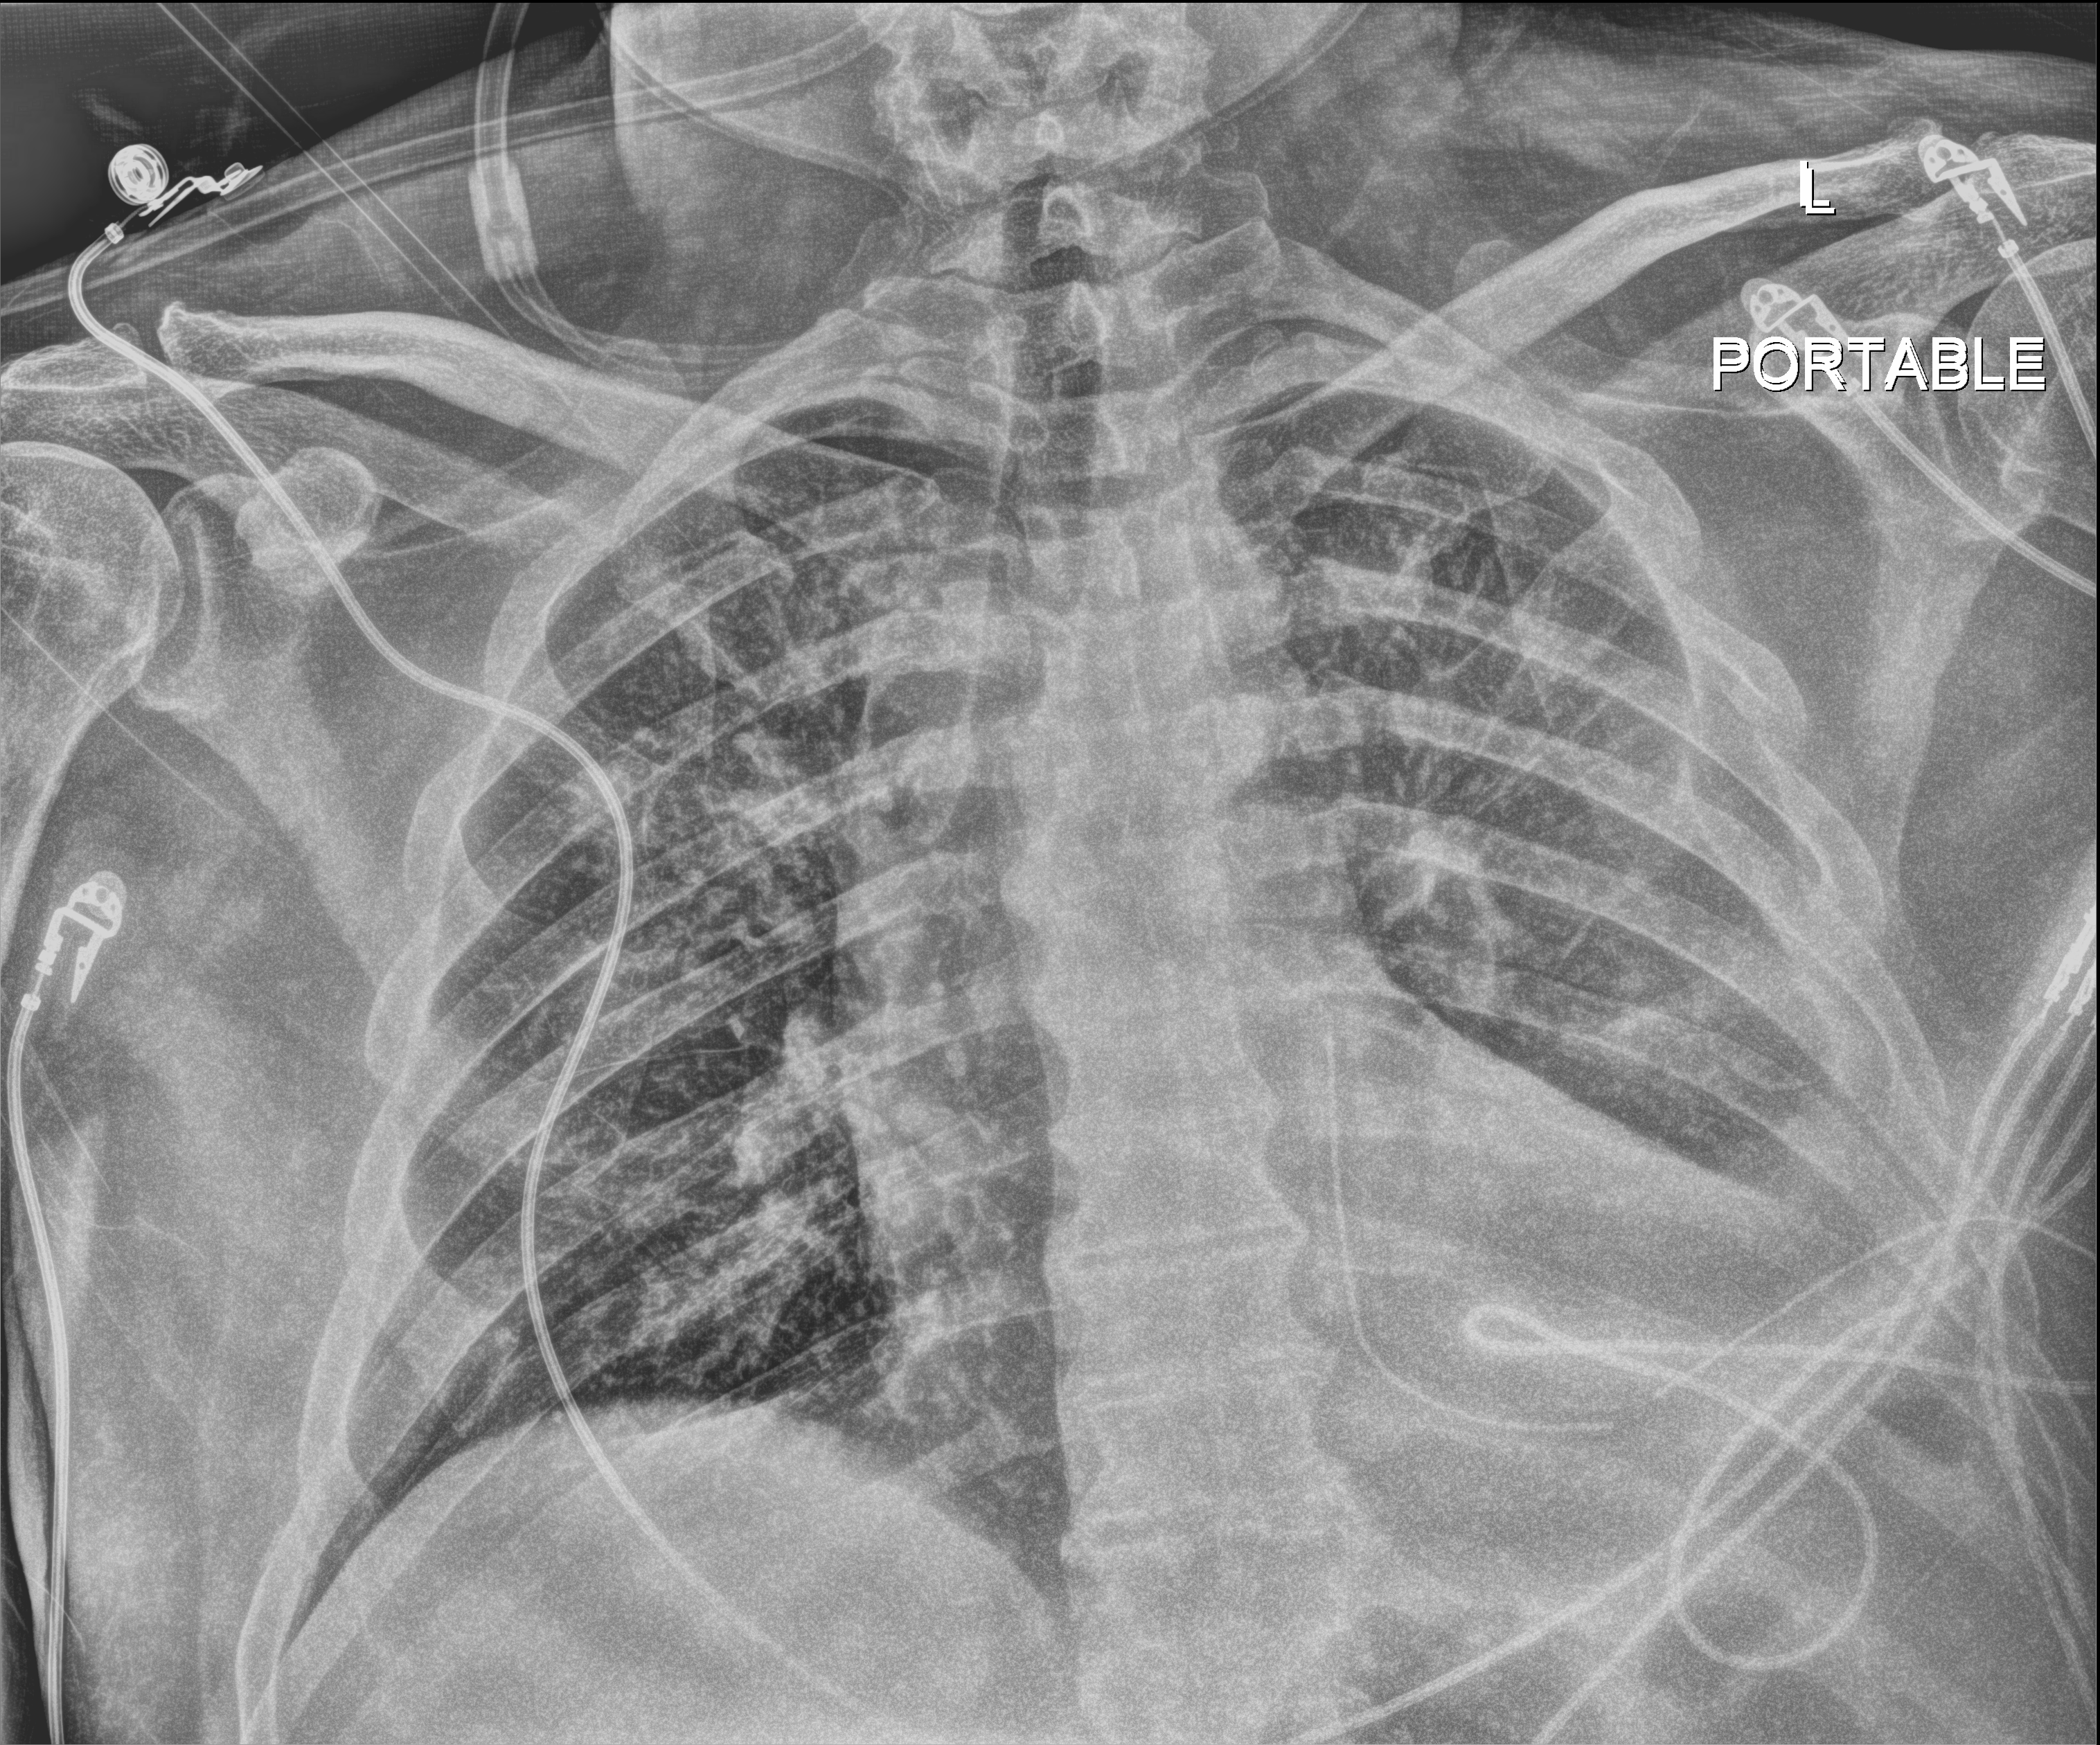
Chest X-ray (portable). Patient hospitalised with COVID-19; male, aged 18–59 years.
Hospital-stay facts (about this admission, not read from this image; timing relative to this image not recorded):
- admitted to intensive care during this hospital stay: no
- mechanically ventilated during this hospital stay: no